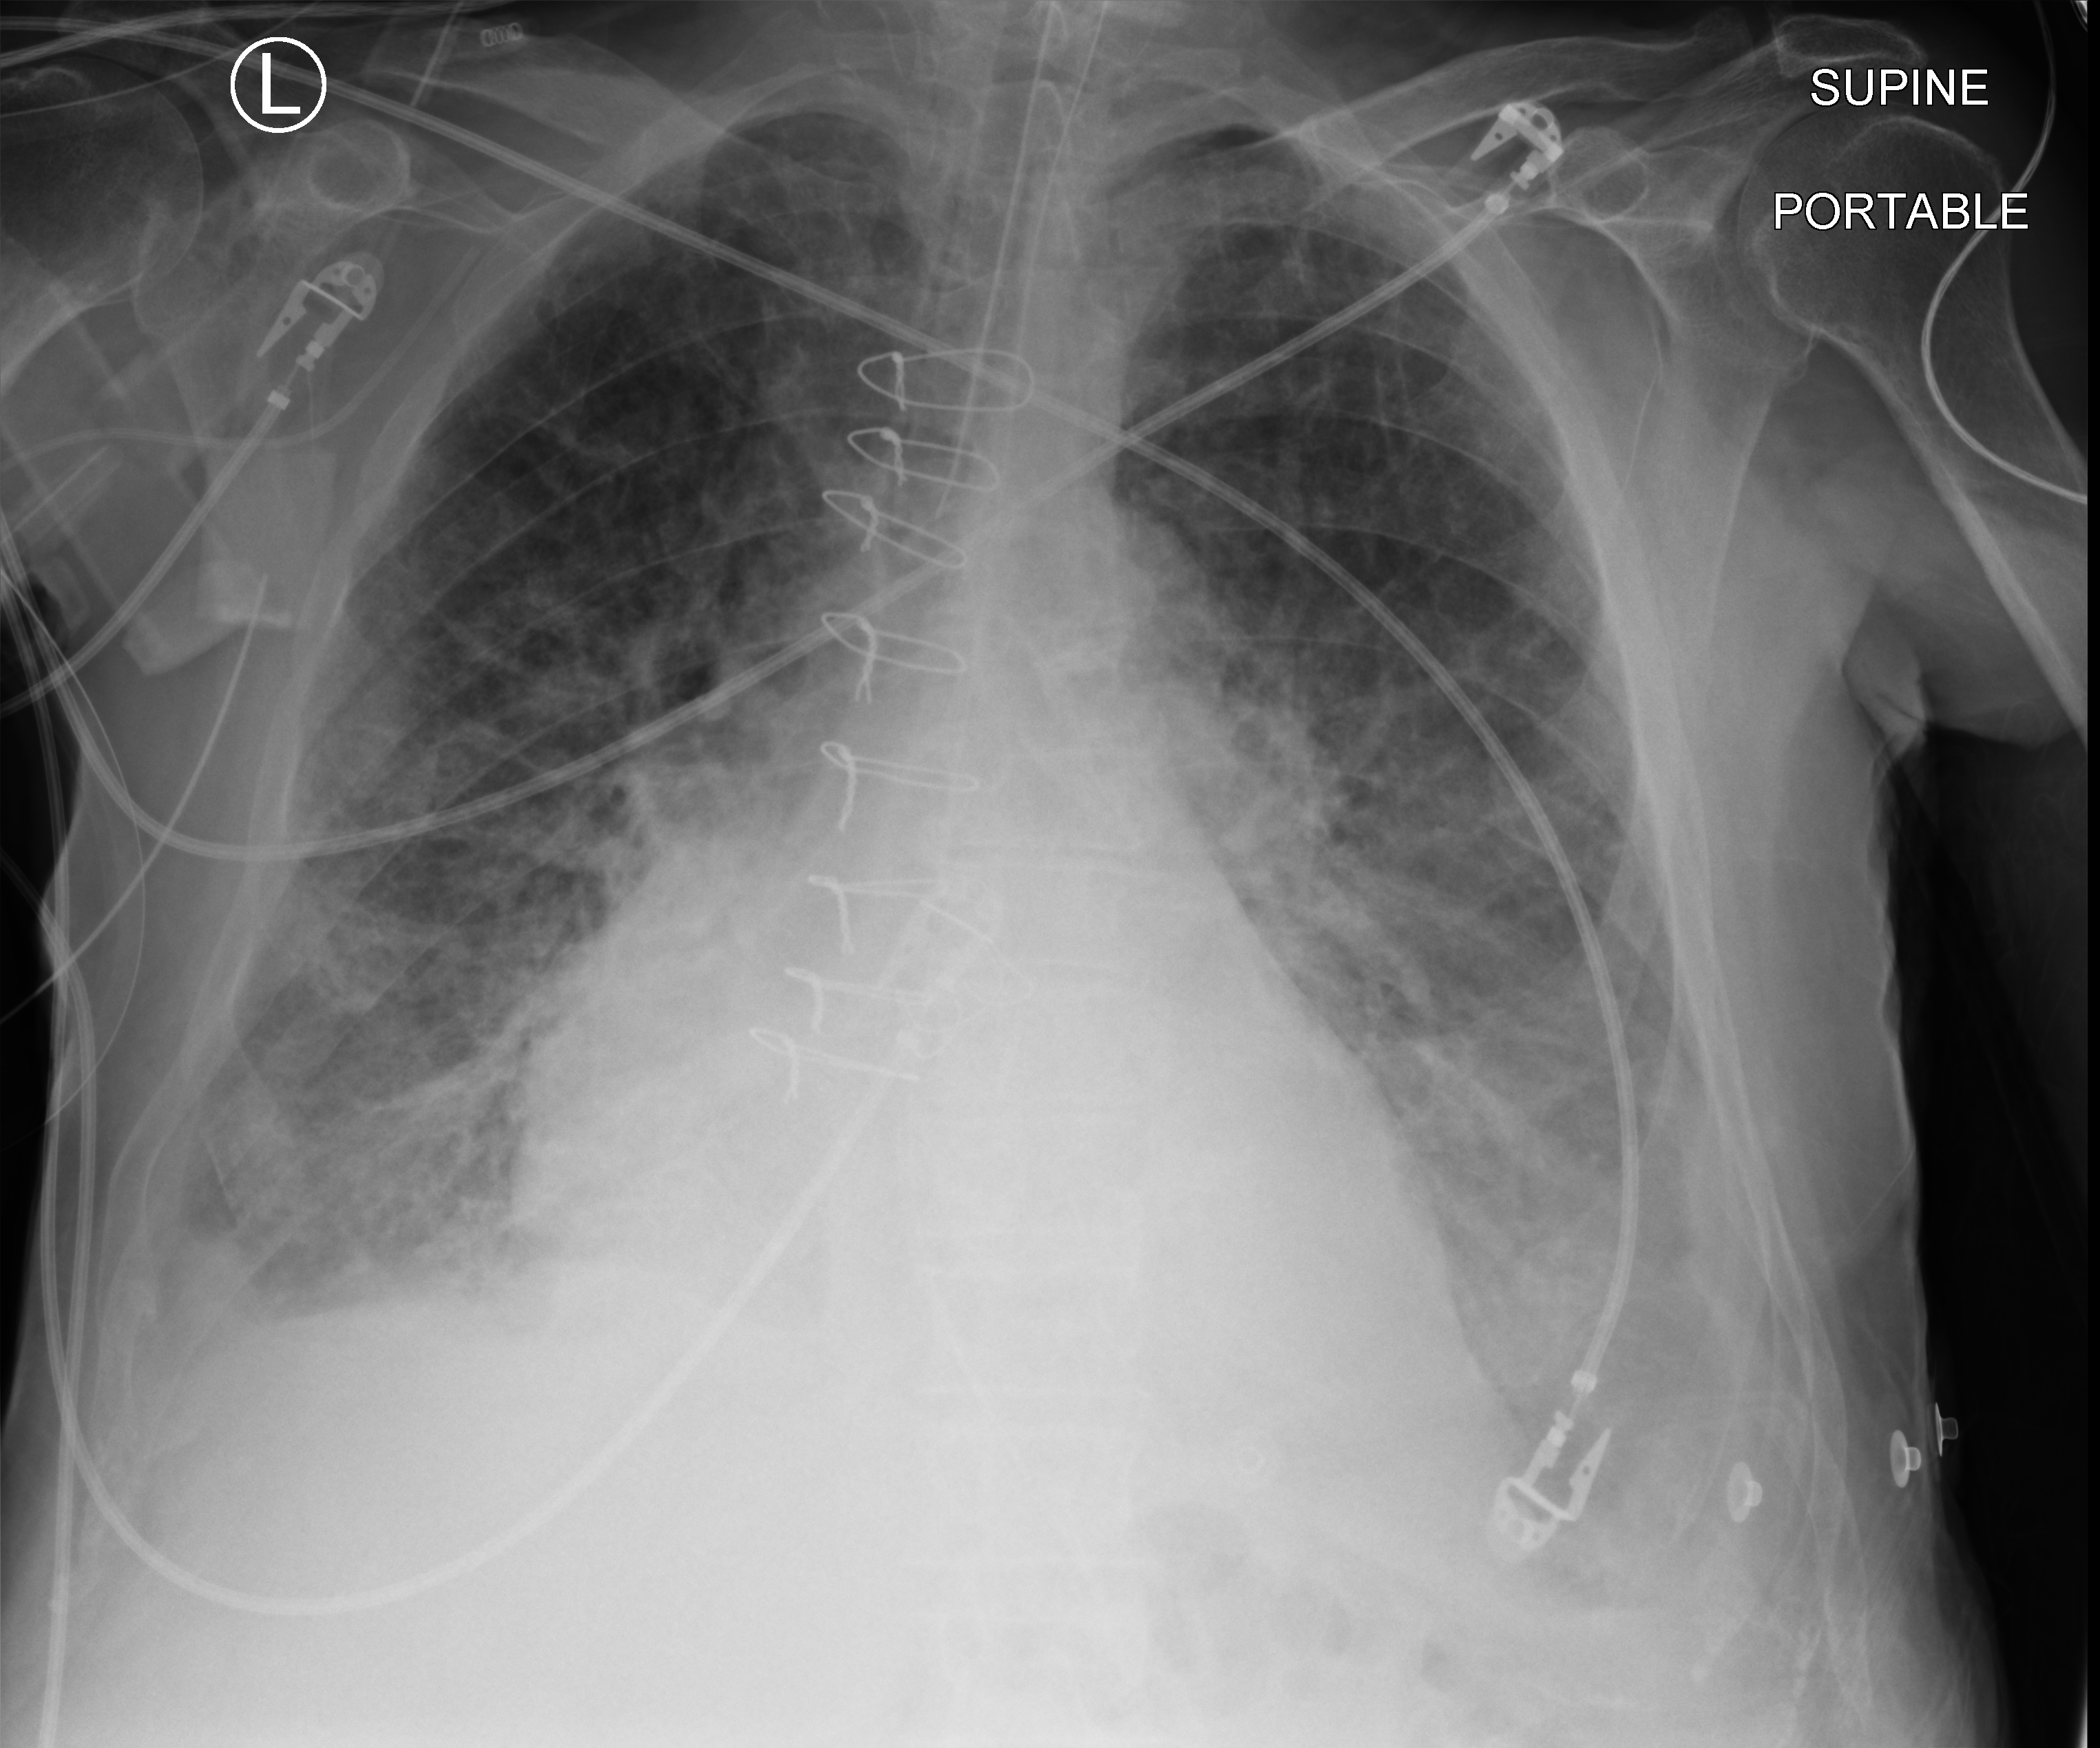
Chest X-ray (portable); anteroposterior (AP) projection. Male patient hospitalised with COVID-19, age 75–90 years.
Admission-level facts for this patient (not findings on this image; timing relative to this image not recorded):
- admitted to intensive care during this hospital stay: yes